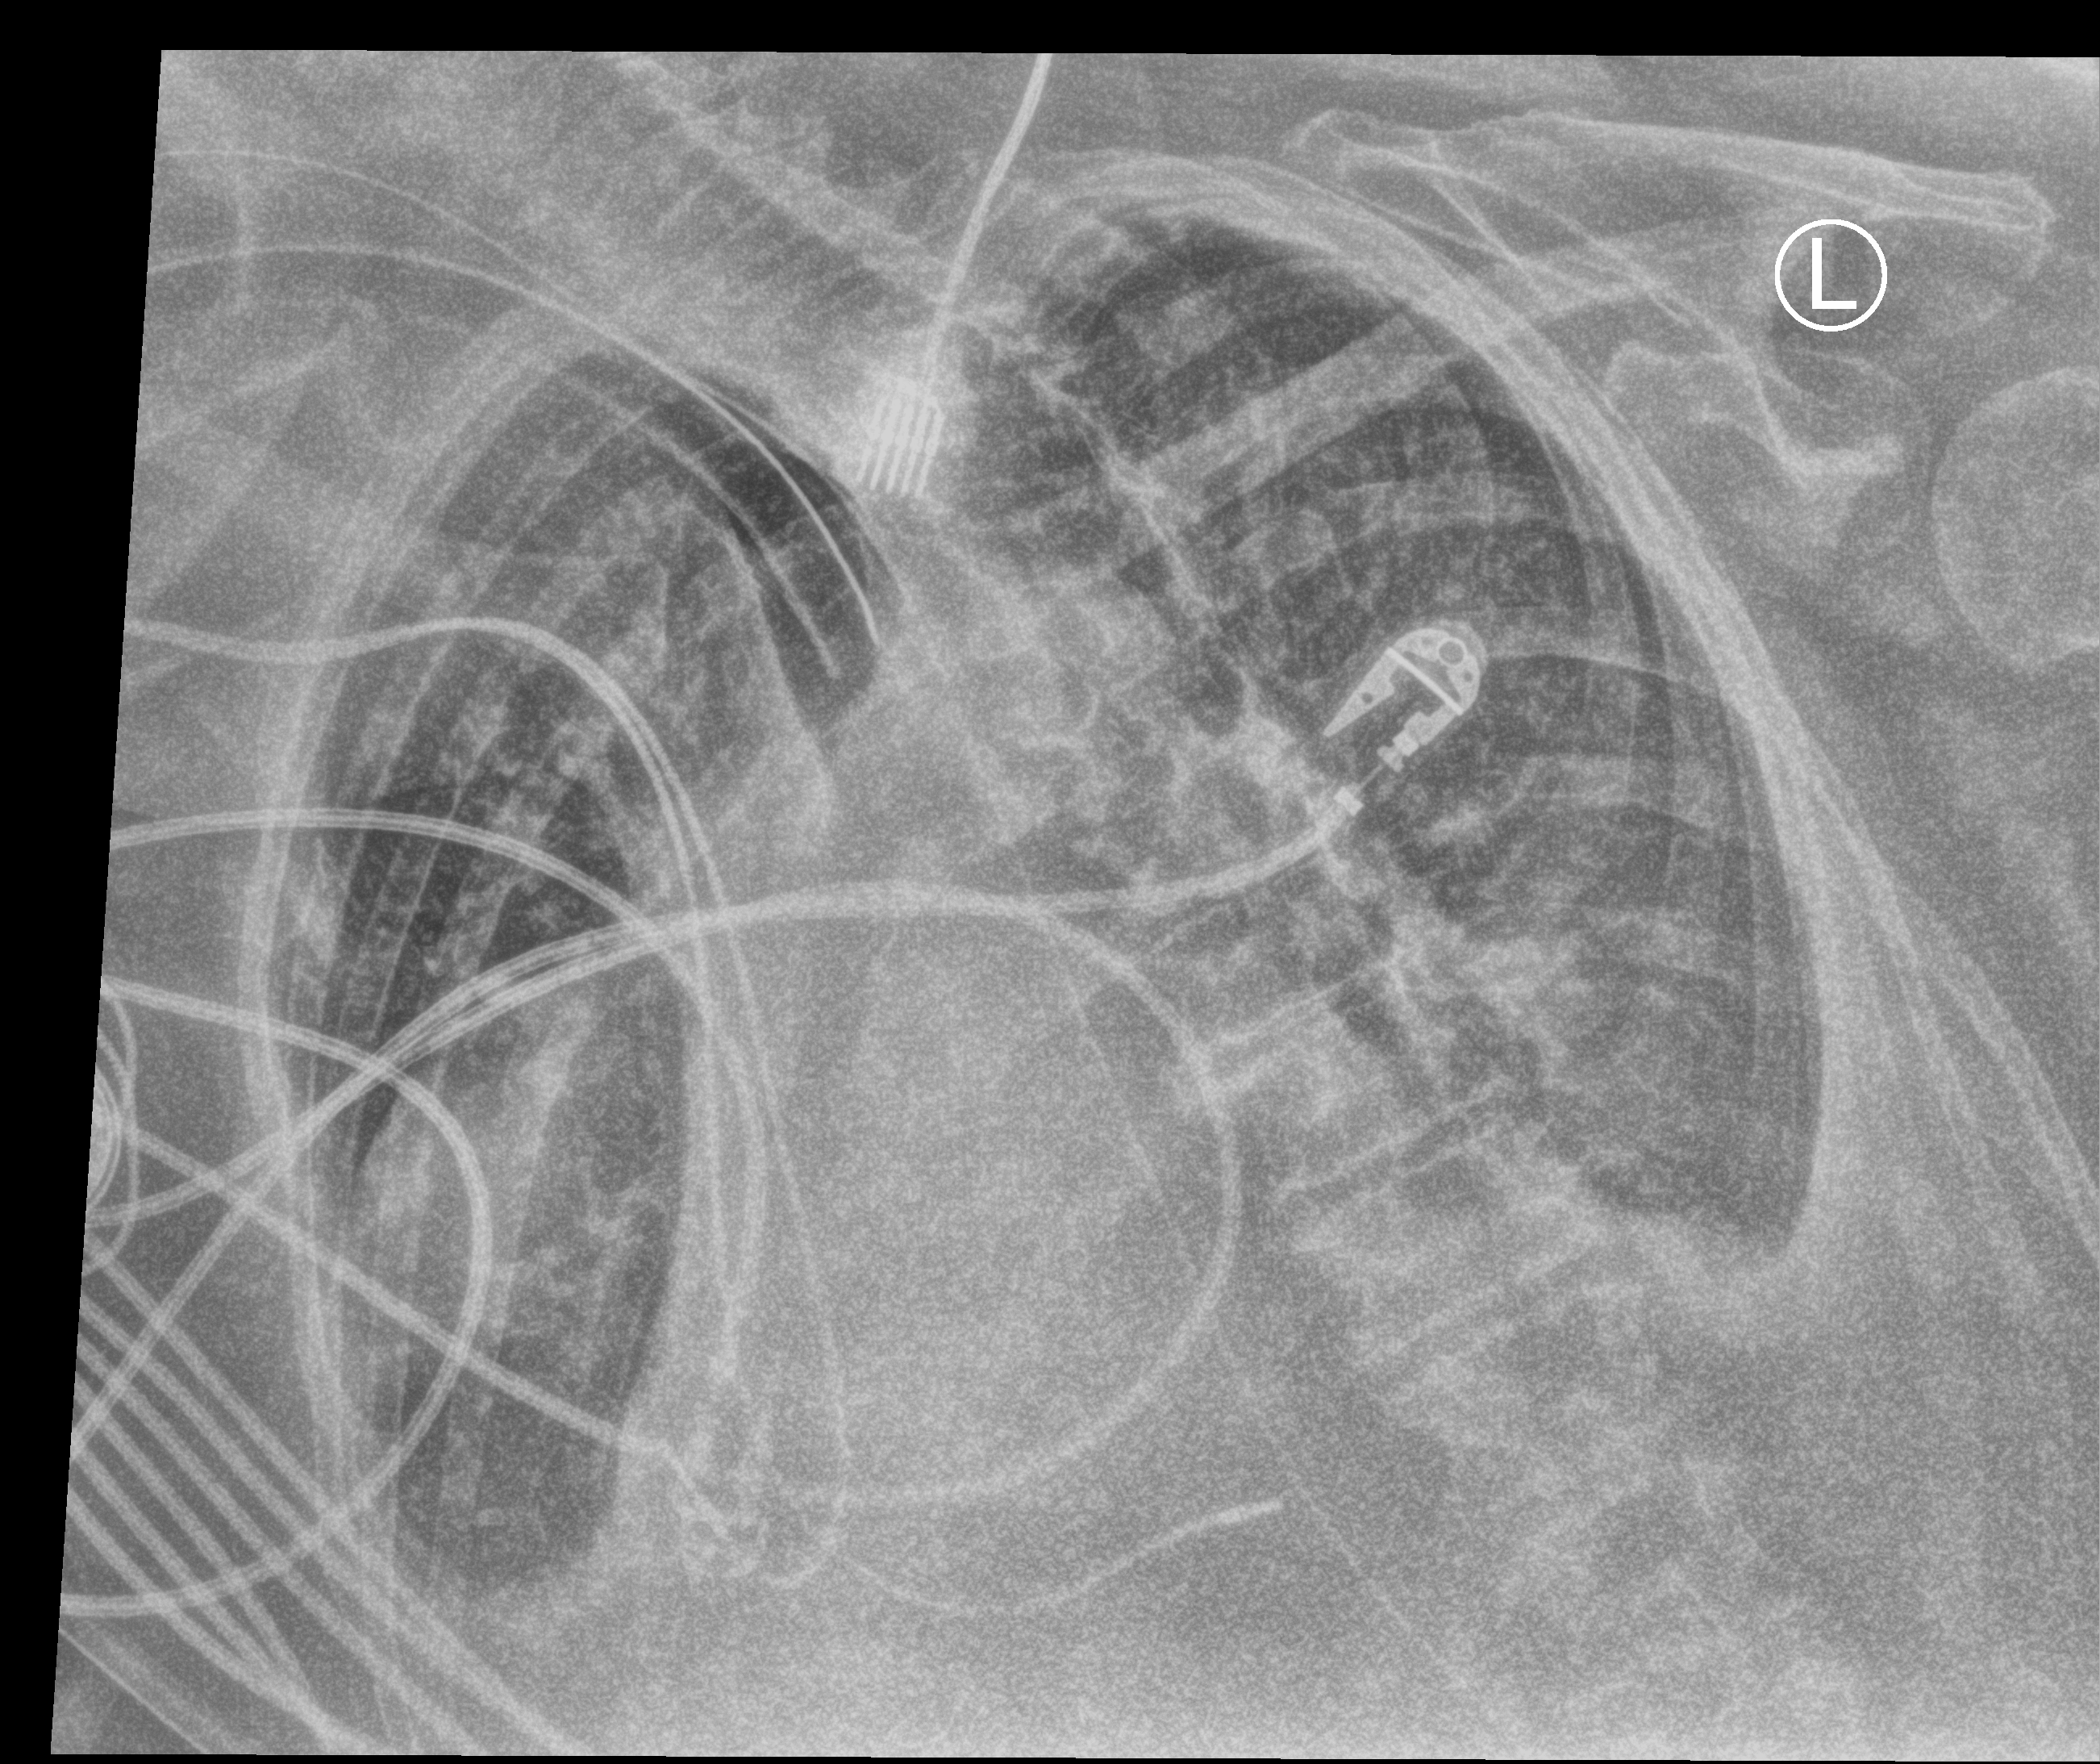
Bedside chest radiograph (computed radiography), anteroposterior (AP) projection. Patient hospitalised with COVID-19; female, aged 75–90 years.
Hospital-stay facts (about this admission, not read from this image; timing relative to this image not recorded): chronic kidney disease (admission record): yes; mechanically ventilated during this hospital stay: yes.